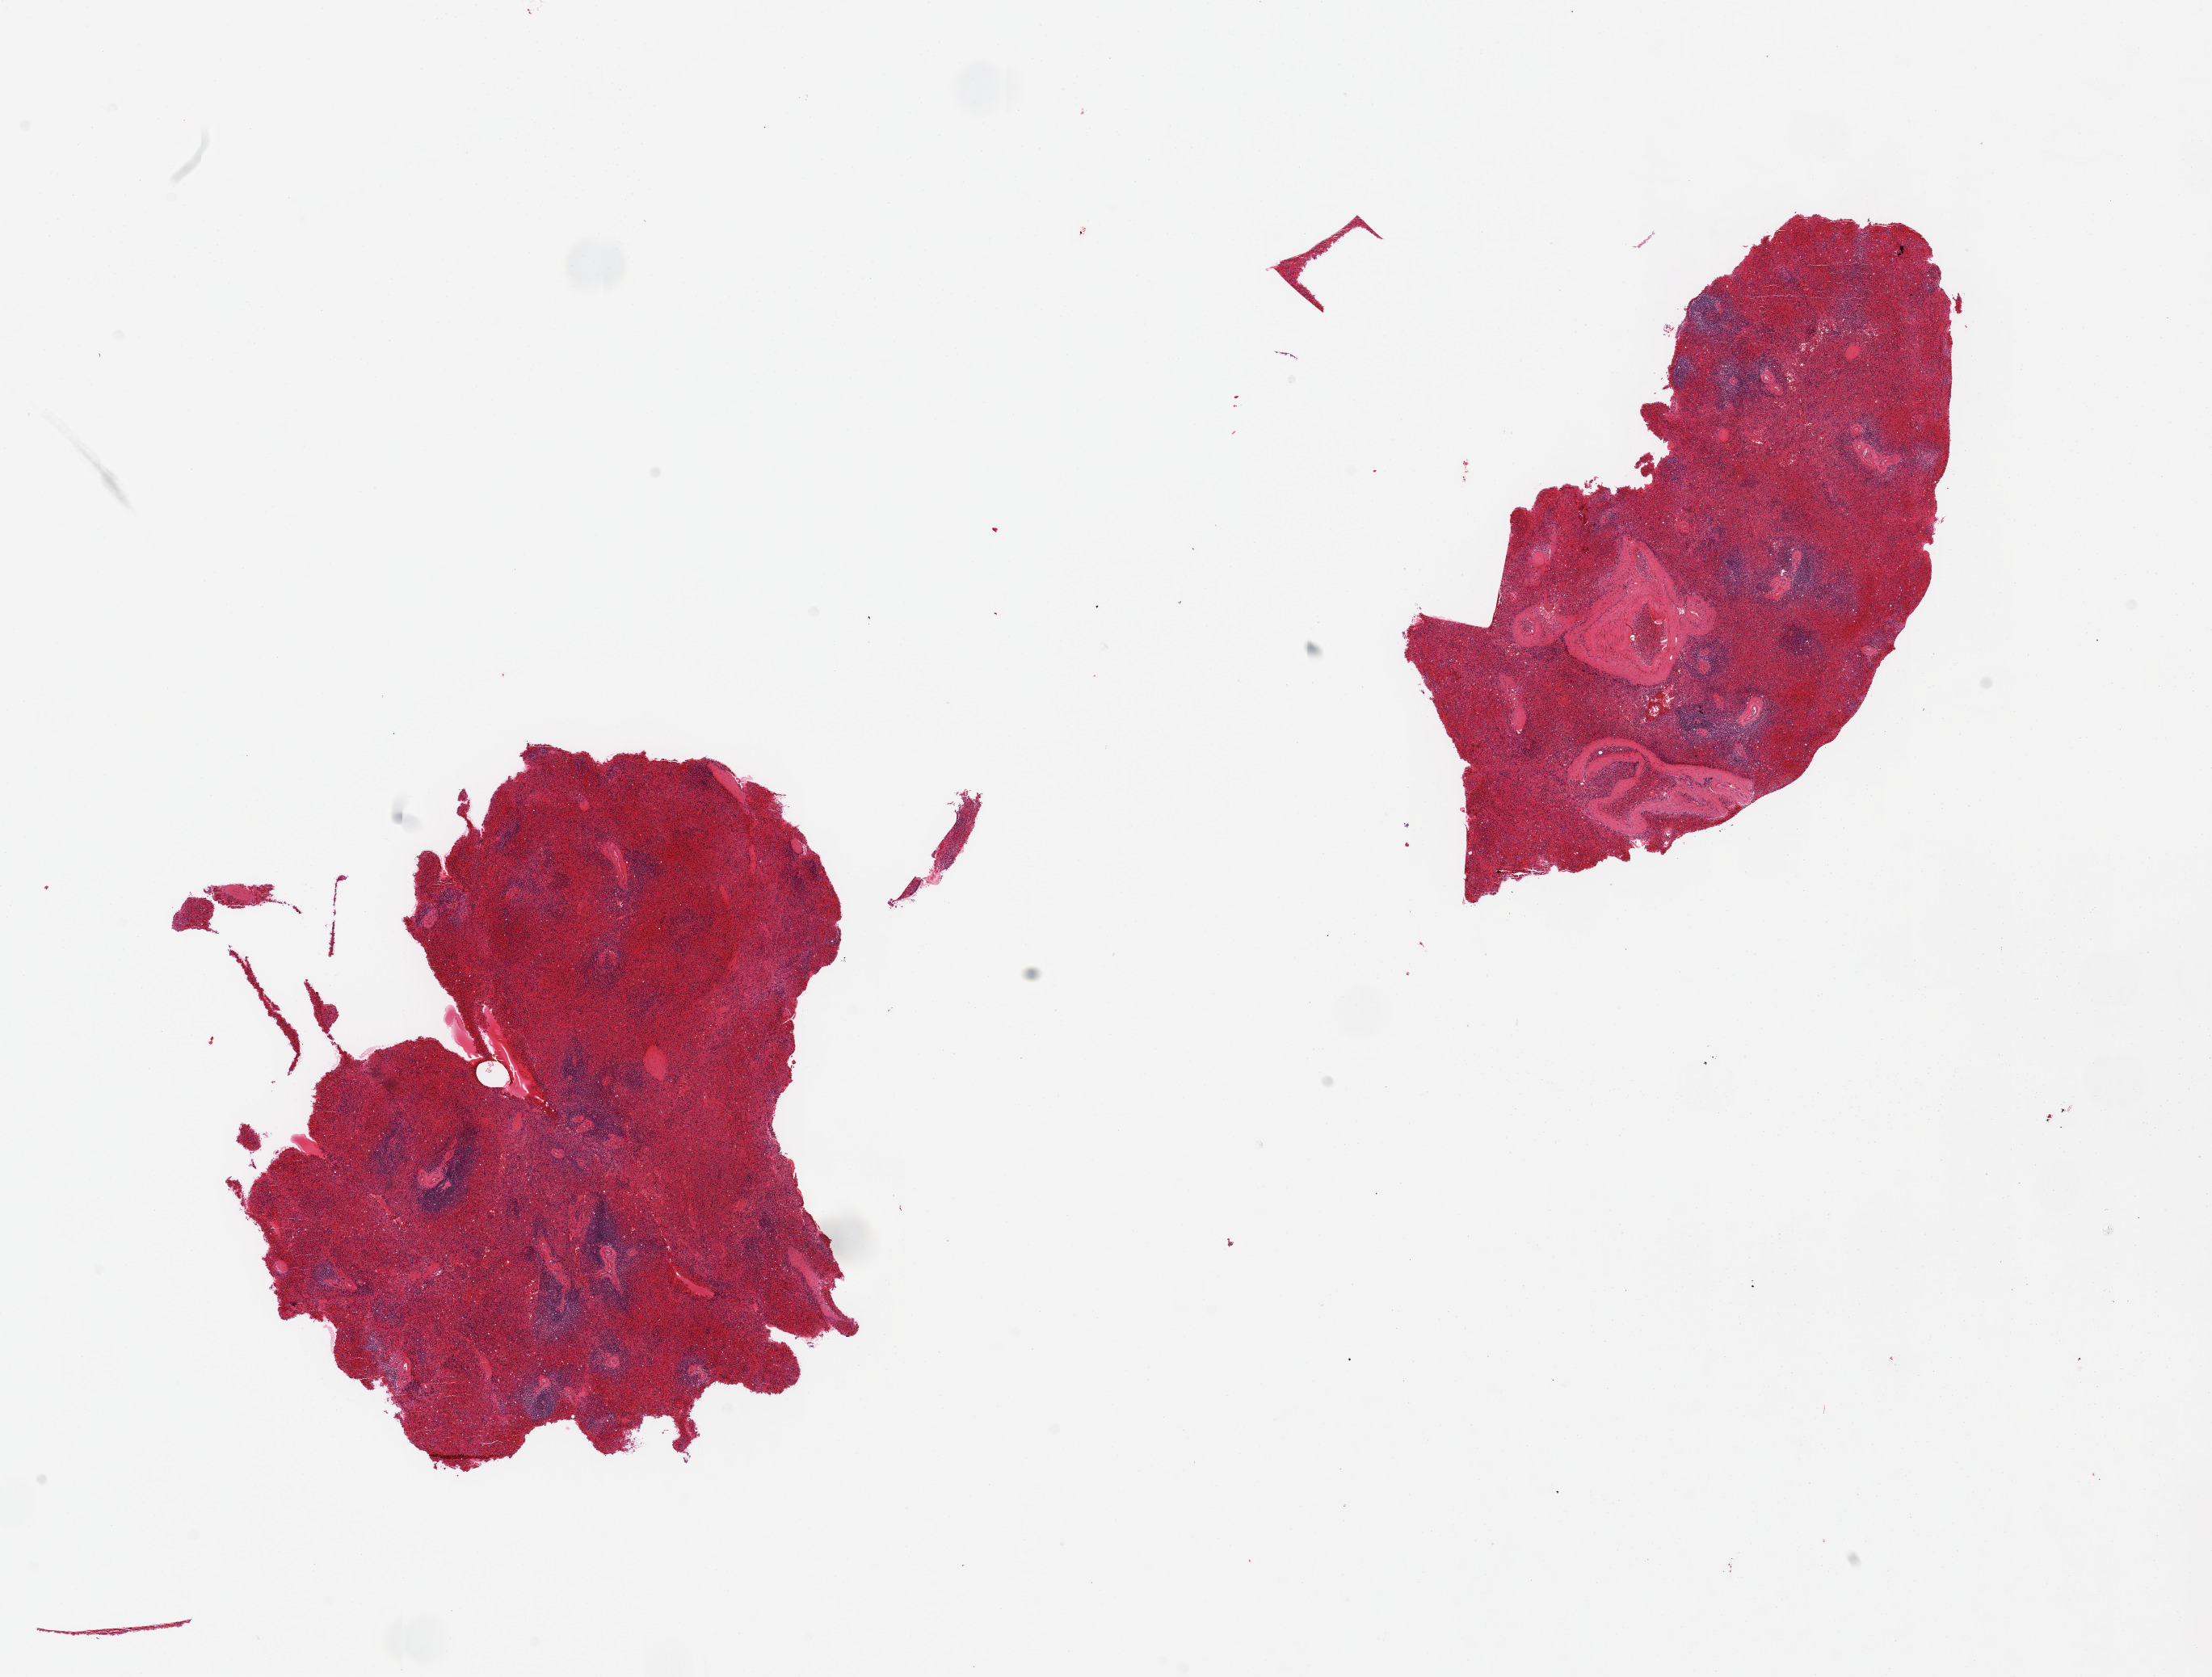
Haematoxylin and eosin whole-slide image — a low-resolution overview of the entire scanned area, about 21.7 x 16.4 mm (from a 20x scan). PAXgene-fixed, paraffin-embedded tissue. Target tissue: spleen. Tissue donor sample. Donor sex: male.
Pathologist's review note for this sample: 2 pieces, congested.